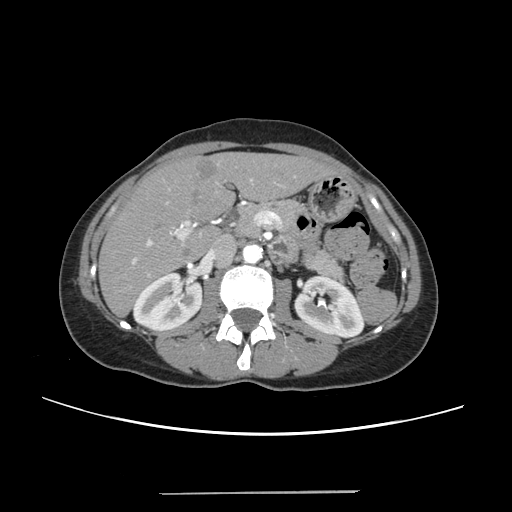
Contrast-enhanced abdominal CT, one axial slice. Position 121 of 240 along the scan axis. Intravenous contrast given. Soft-tissue window (W 400 / L 40 HU). 1.25 mm slice thickness. 512 × 512 image matrix, field of view 371 × 371 mm. Female patient, age 60 years. Case-level facts recorded for this patient, not image findings: diagnosis: colorectal cancer liver metastases, imaged before liver resection; multiple liver metastases: no; largest metastasis: 1.5 cm; disease in both lobes: no.
Annotated regions visible in this slice (outlined manually by an expert reader):
- liver: bounding box <101,153,329,314> (left, top, right, bottom; pixels)
- planned liver remnant (the part of the liver to remain after resection): <100,154,329,314>
- portal vein (with intrahepatic branches): <132,179,276,276>
- liver metastasis: <196,160,218,181>